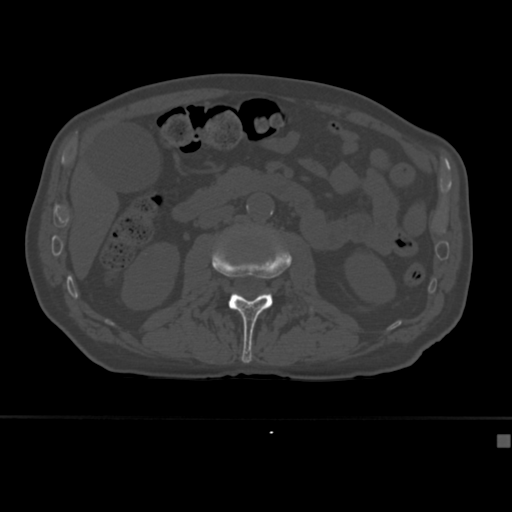
CT including the spine, one axial slice; slice 144 of 430 in the series (ordered by position); reconstruction kernel Br40s; 120 kVp; bone window (W 1800 / L 400 HU); 512 × 512 image matrix. Patient: male, 64 years. From the clinical record (not read from this slice): primary cancer: uterus; vertebrae with lytic lesions (as recorded): T1, T4, T5, T7, L5.
Annotated regions visible in this slice (semi-automatically segmented with operator editing):
- L2 vertebra: bounding box [x1, y1, x2, y2] px = [212, 235, 313, 363]